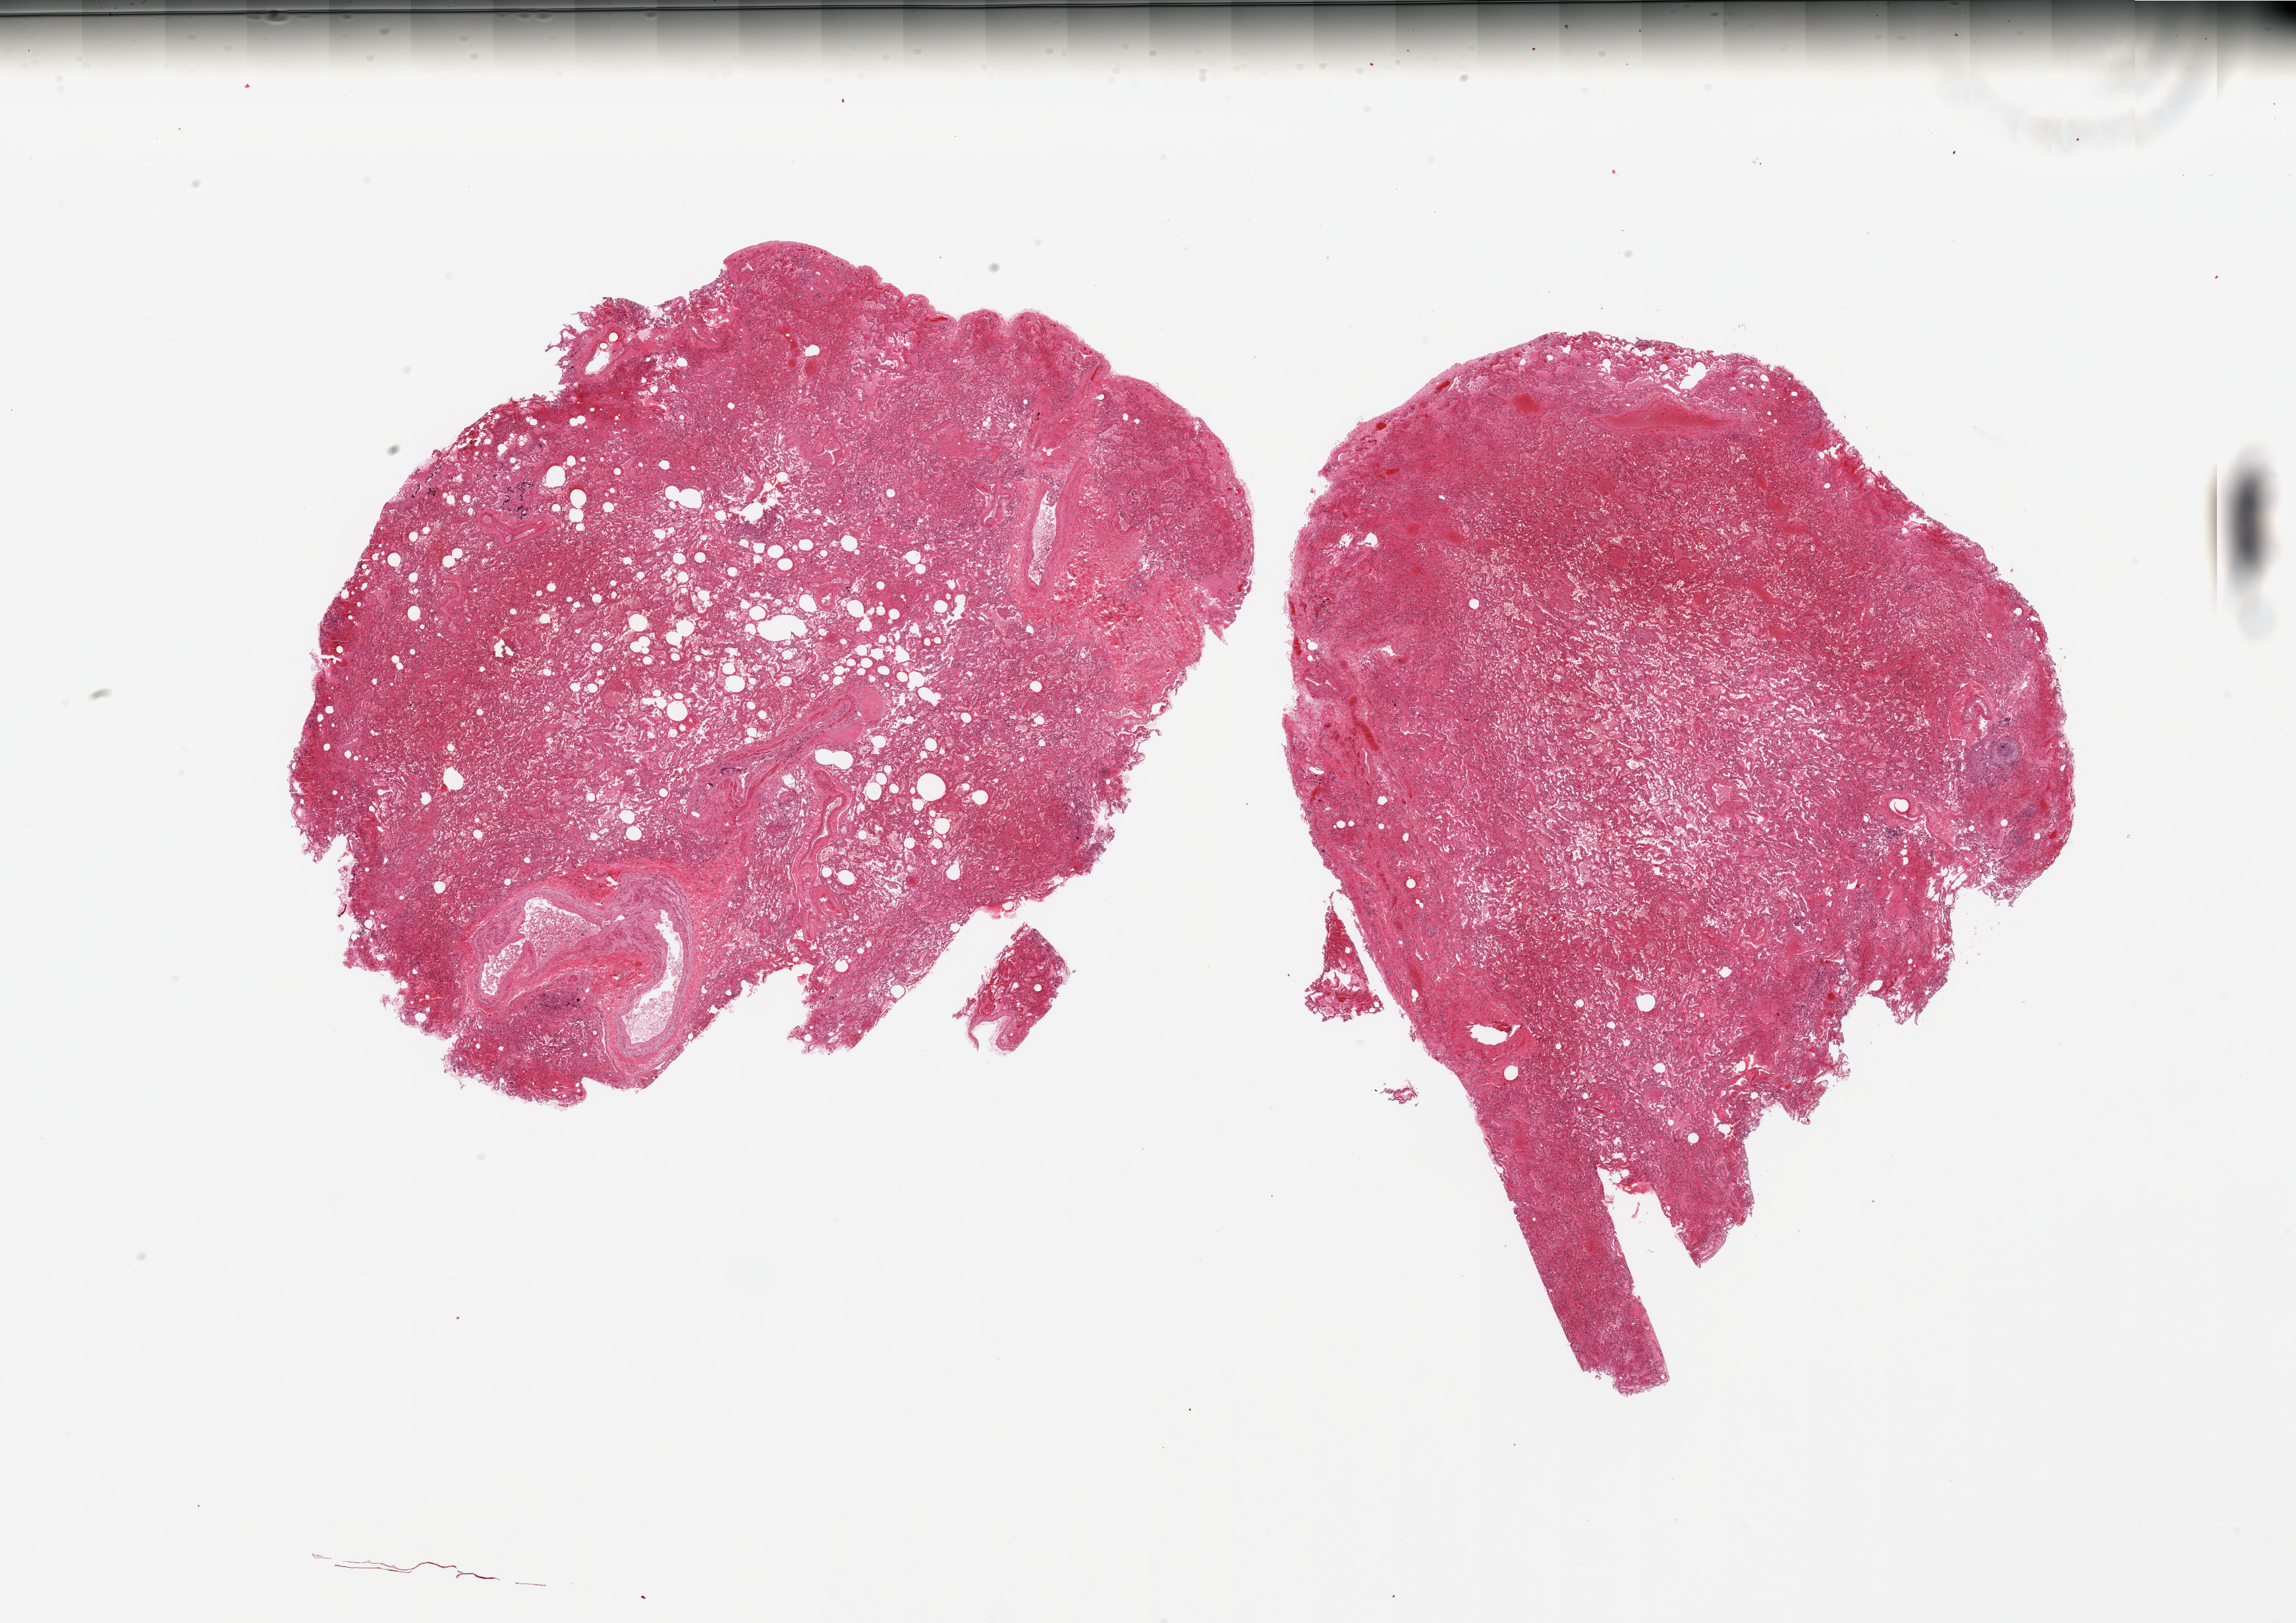
H&E whole-slide image — shown as a low-resolution overview of the whole scanned area (about 27.6 x 19.5 mm, acquisition: 20x scan). PAXgene-fixed, paraffin-embedded tissue. Target tissue: lung. Donor tissue sample.
Pathologist's review note for this sample: 2 pieces marked acute/subacute congestion.